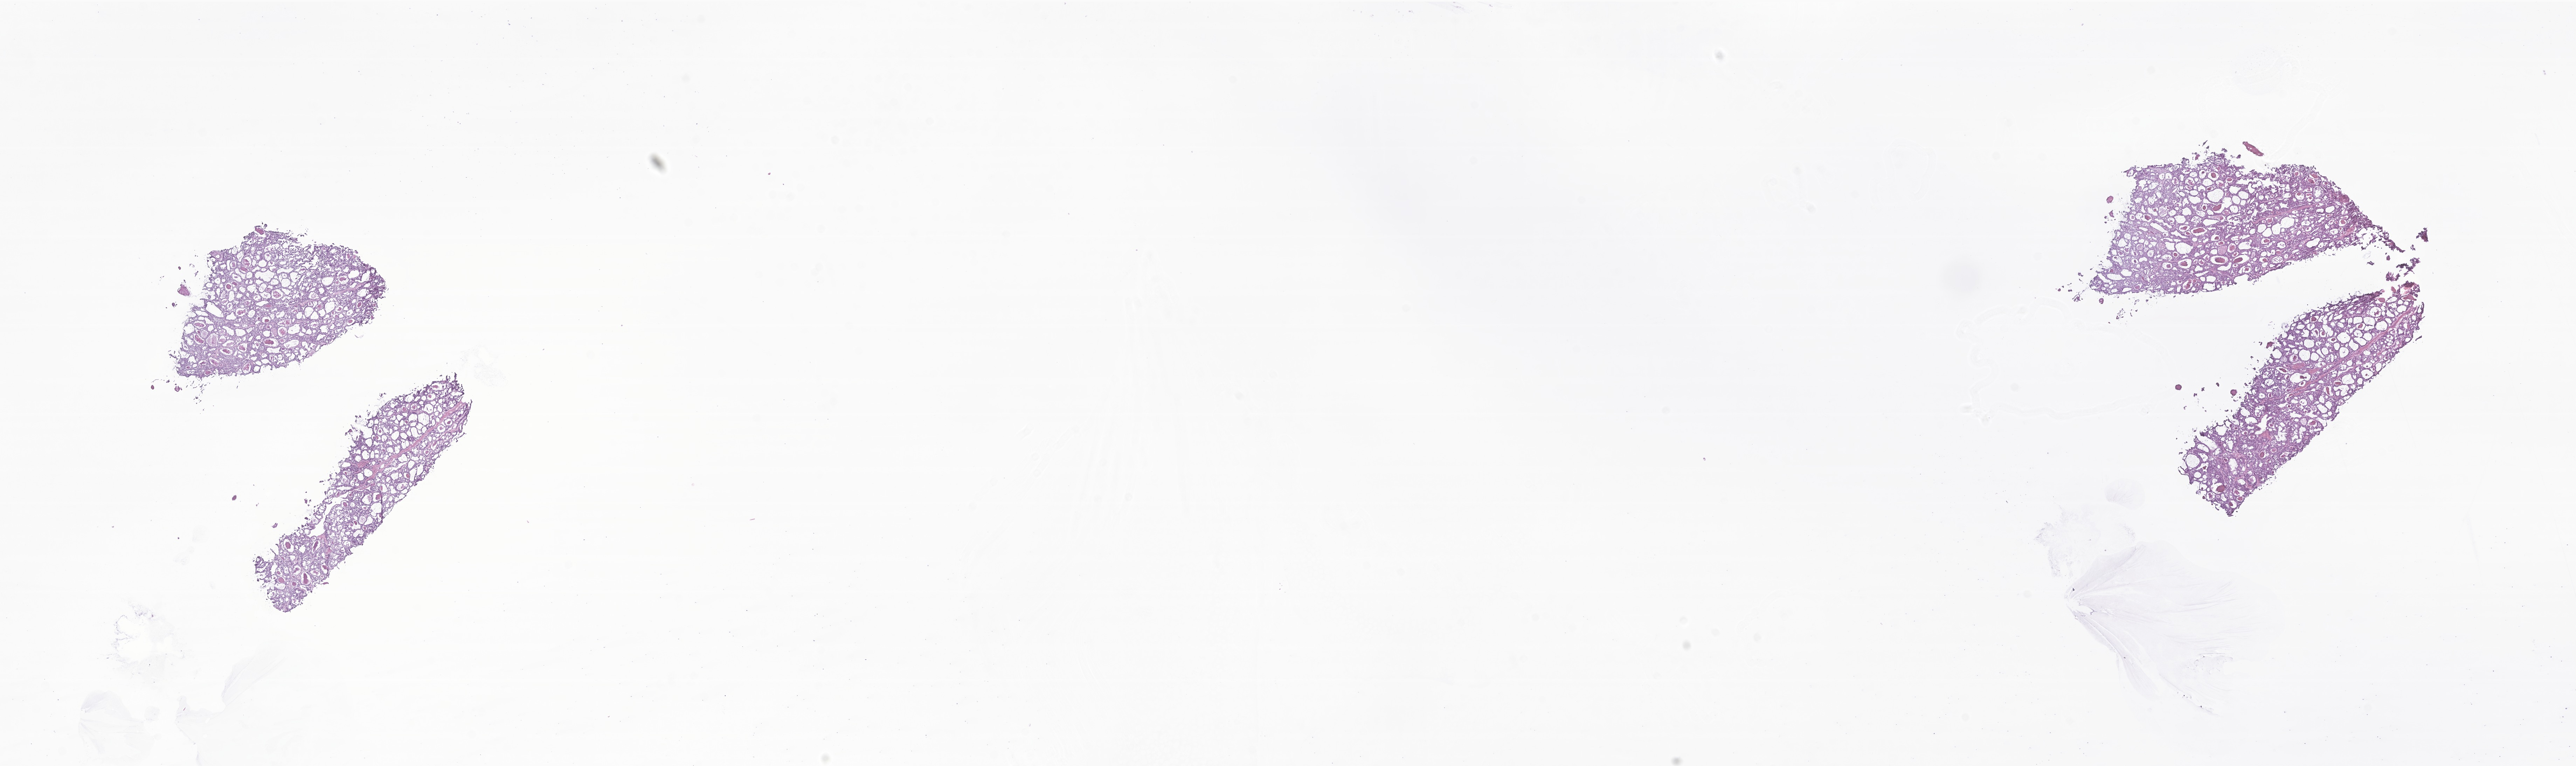
Digitized hematoxylin and eosin (H&E)-stained section of tumor tissue from the thyroid — whole scanned area (about 31.0 x 9.2 mm) shown as a low-resolution overview, frozen section (OCT-embedded). Patient: male, age 227 months (18 years 11 months).
- recorded diagnosis: Papillary carcinoma, NOS